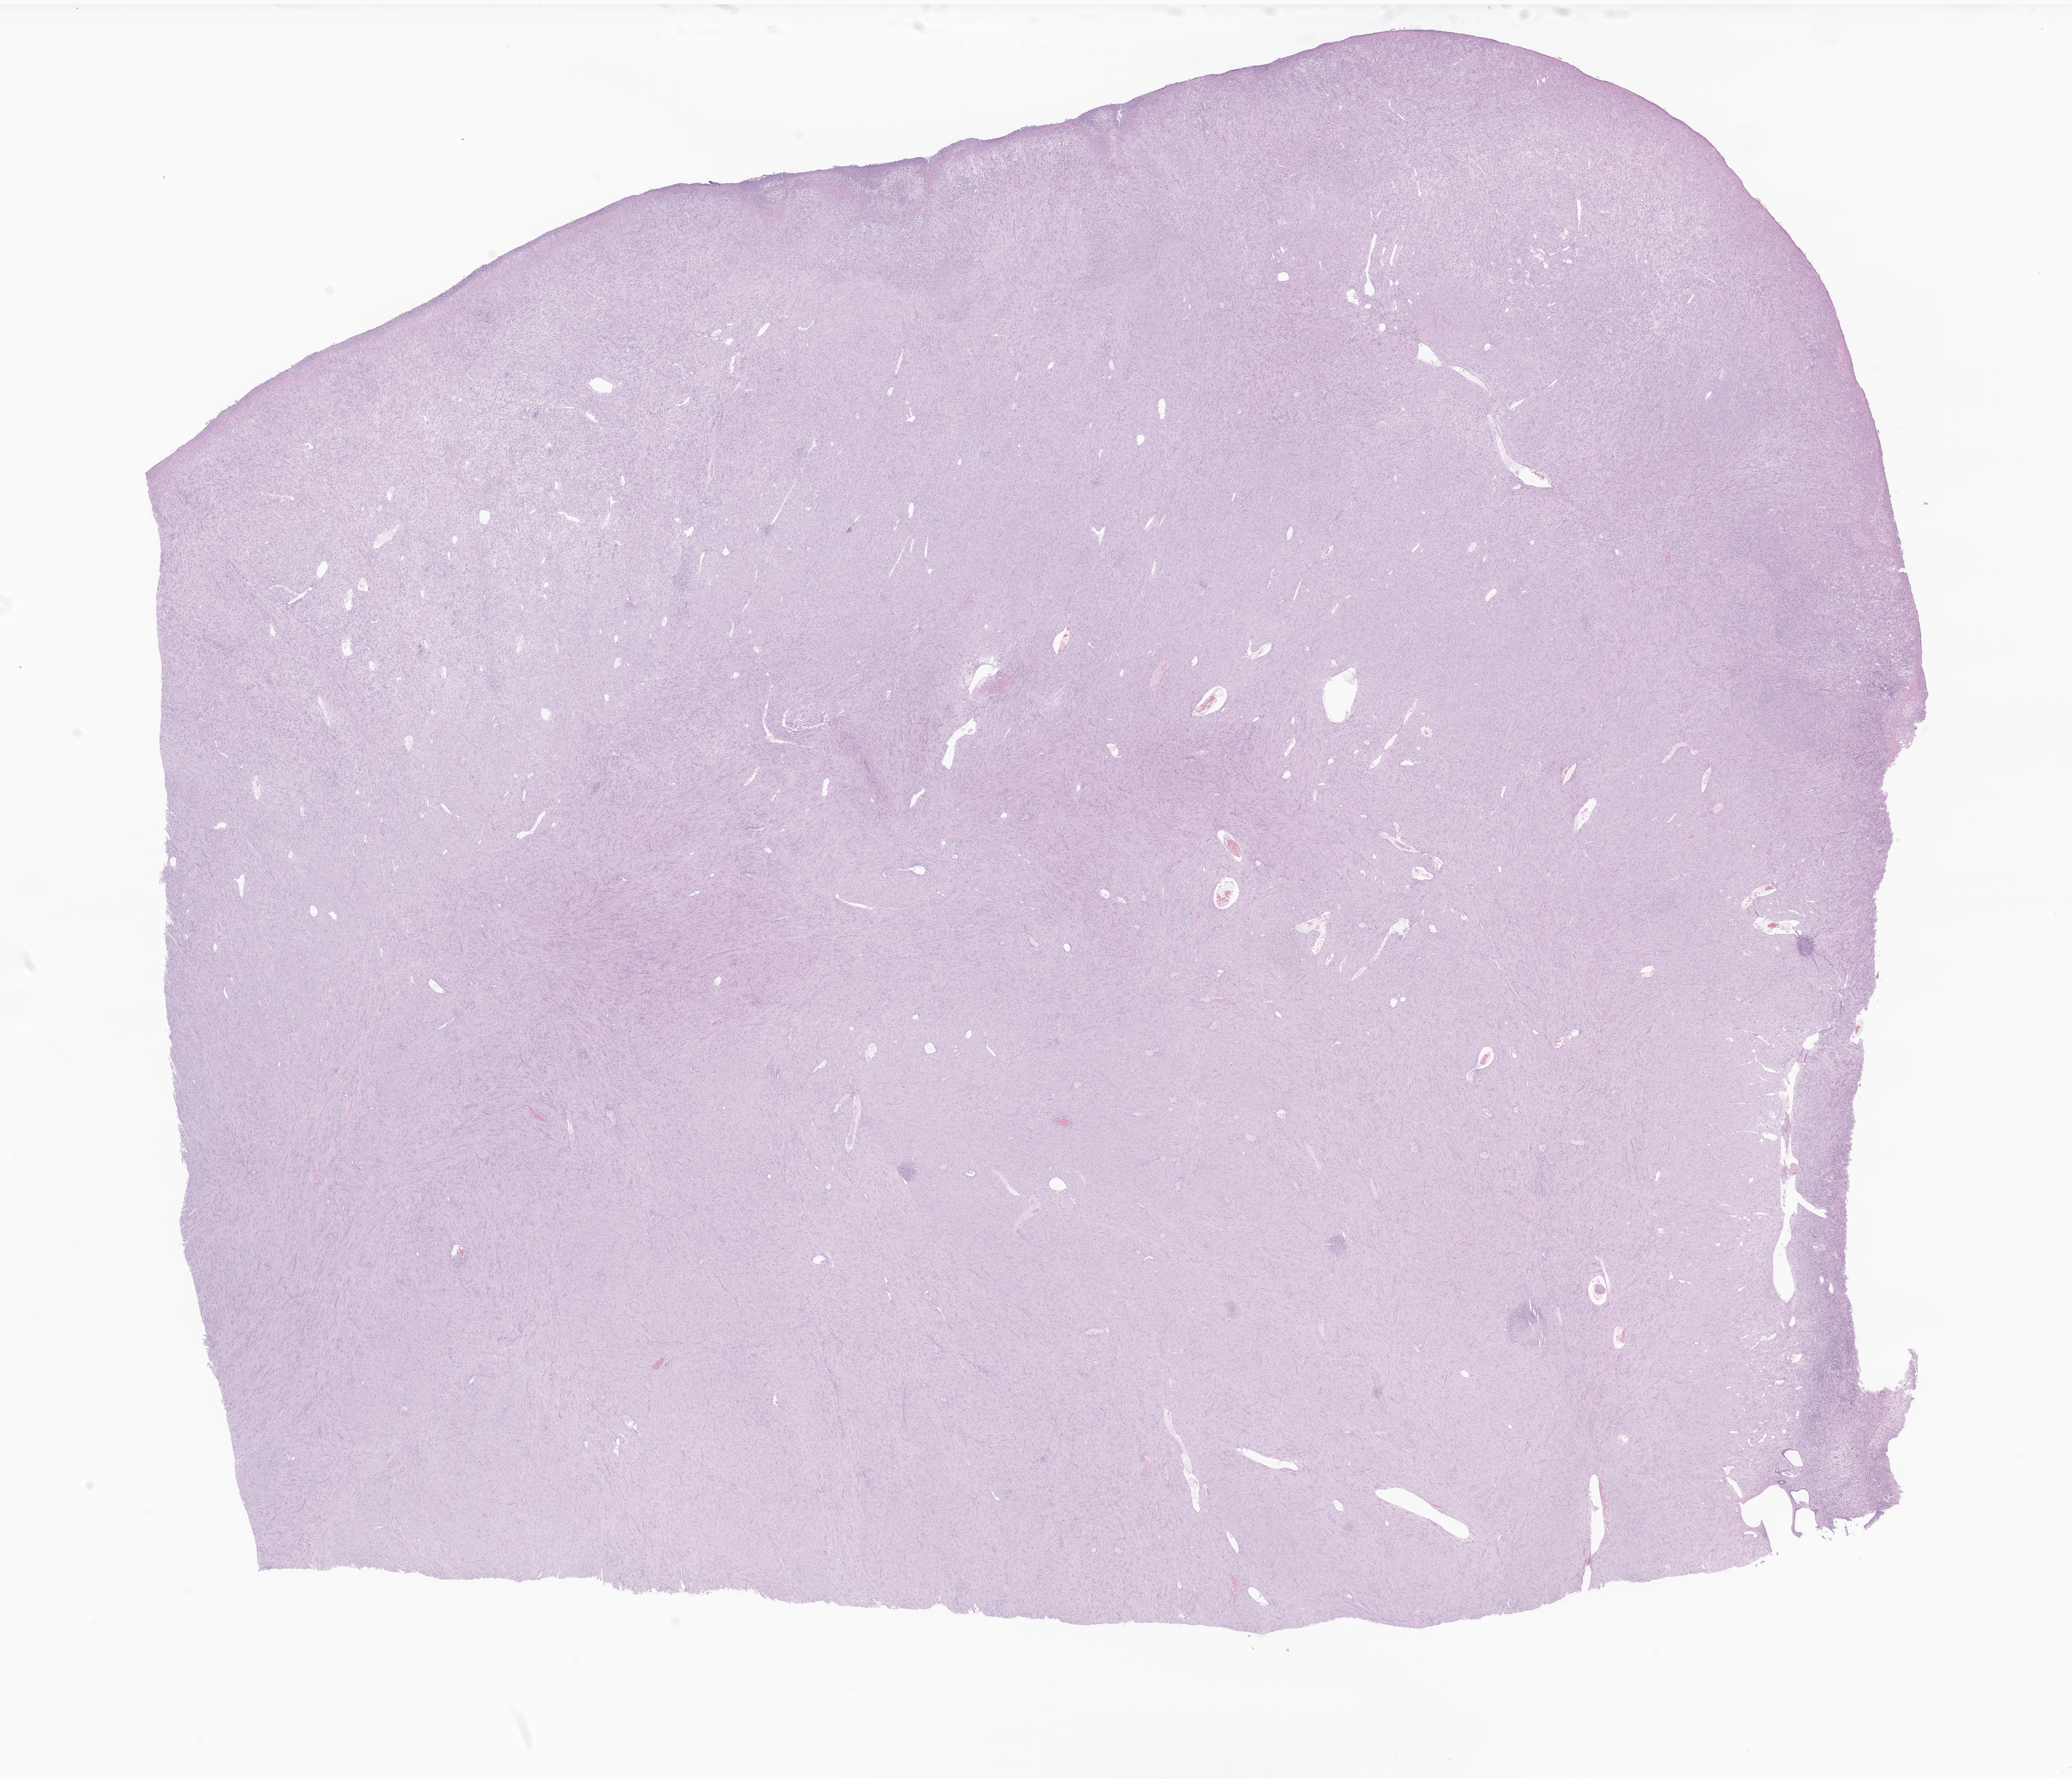
Haematoxylin and eosin whole-slide image of tumor tissue from the cecum — whole scanned area (about 26.4 x 22.7 mm) shown as a low-resolution overview; FFPE section. Patient: female, age 74 months (6 years 2 months).
Recorded diagnosis: Myofibroblastic tumor, NOS.